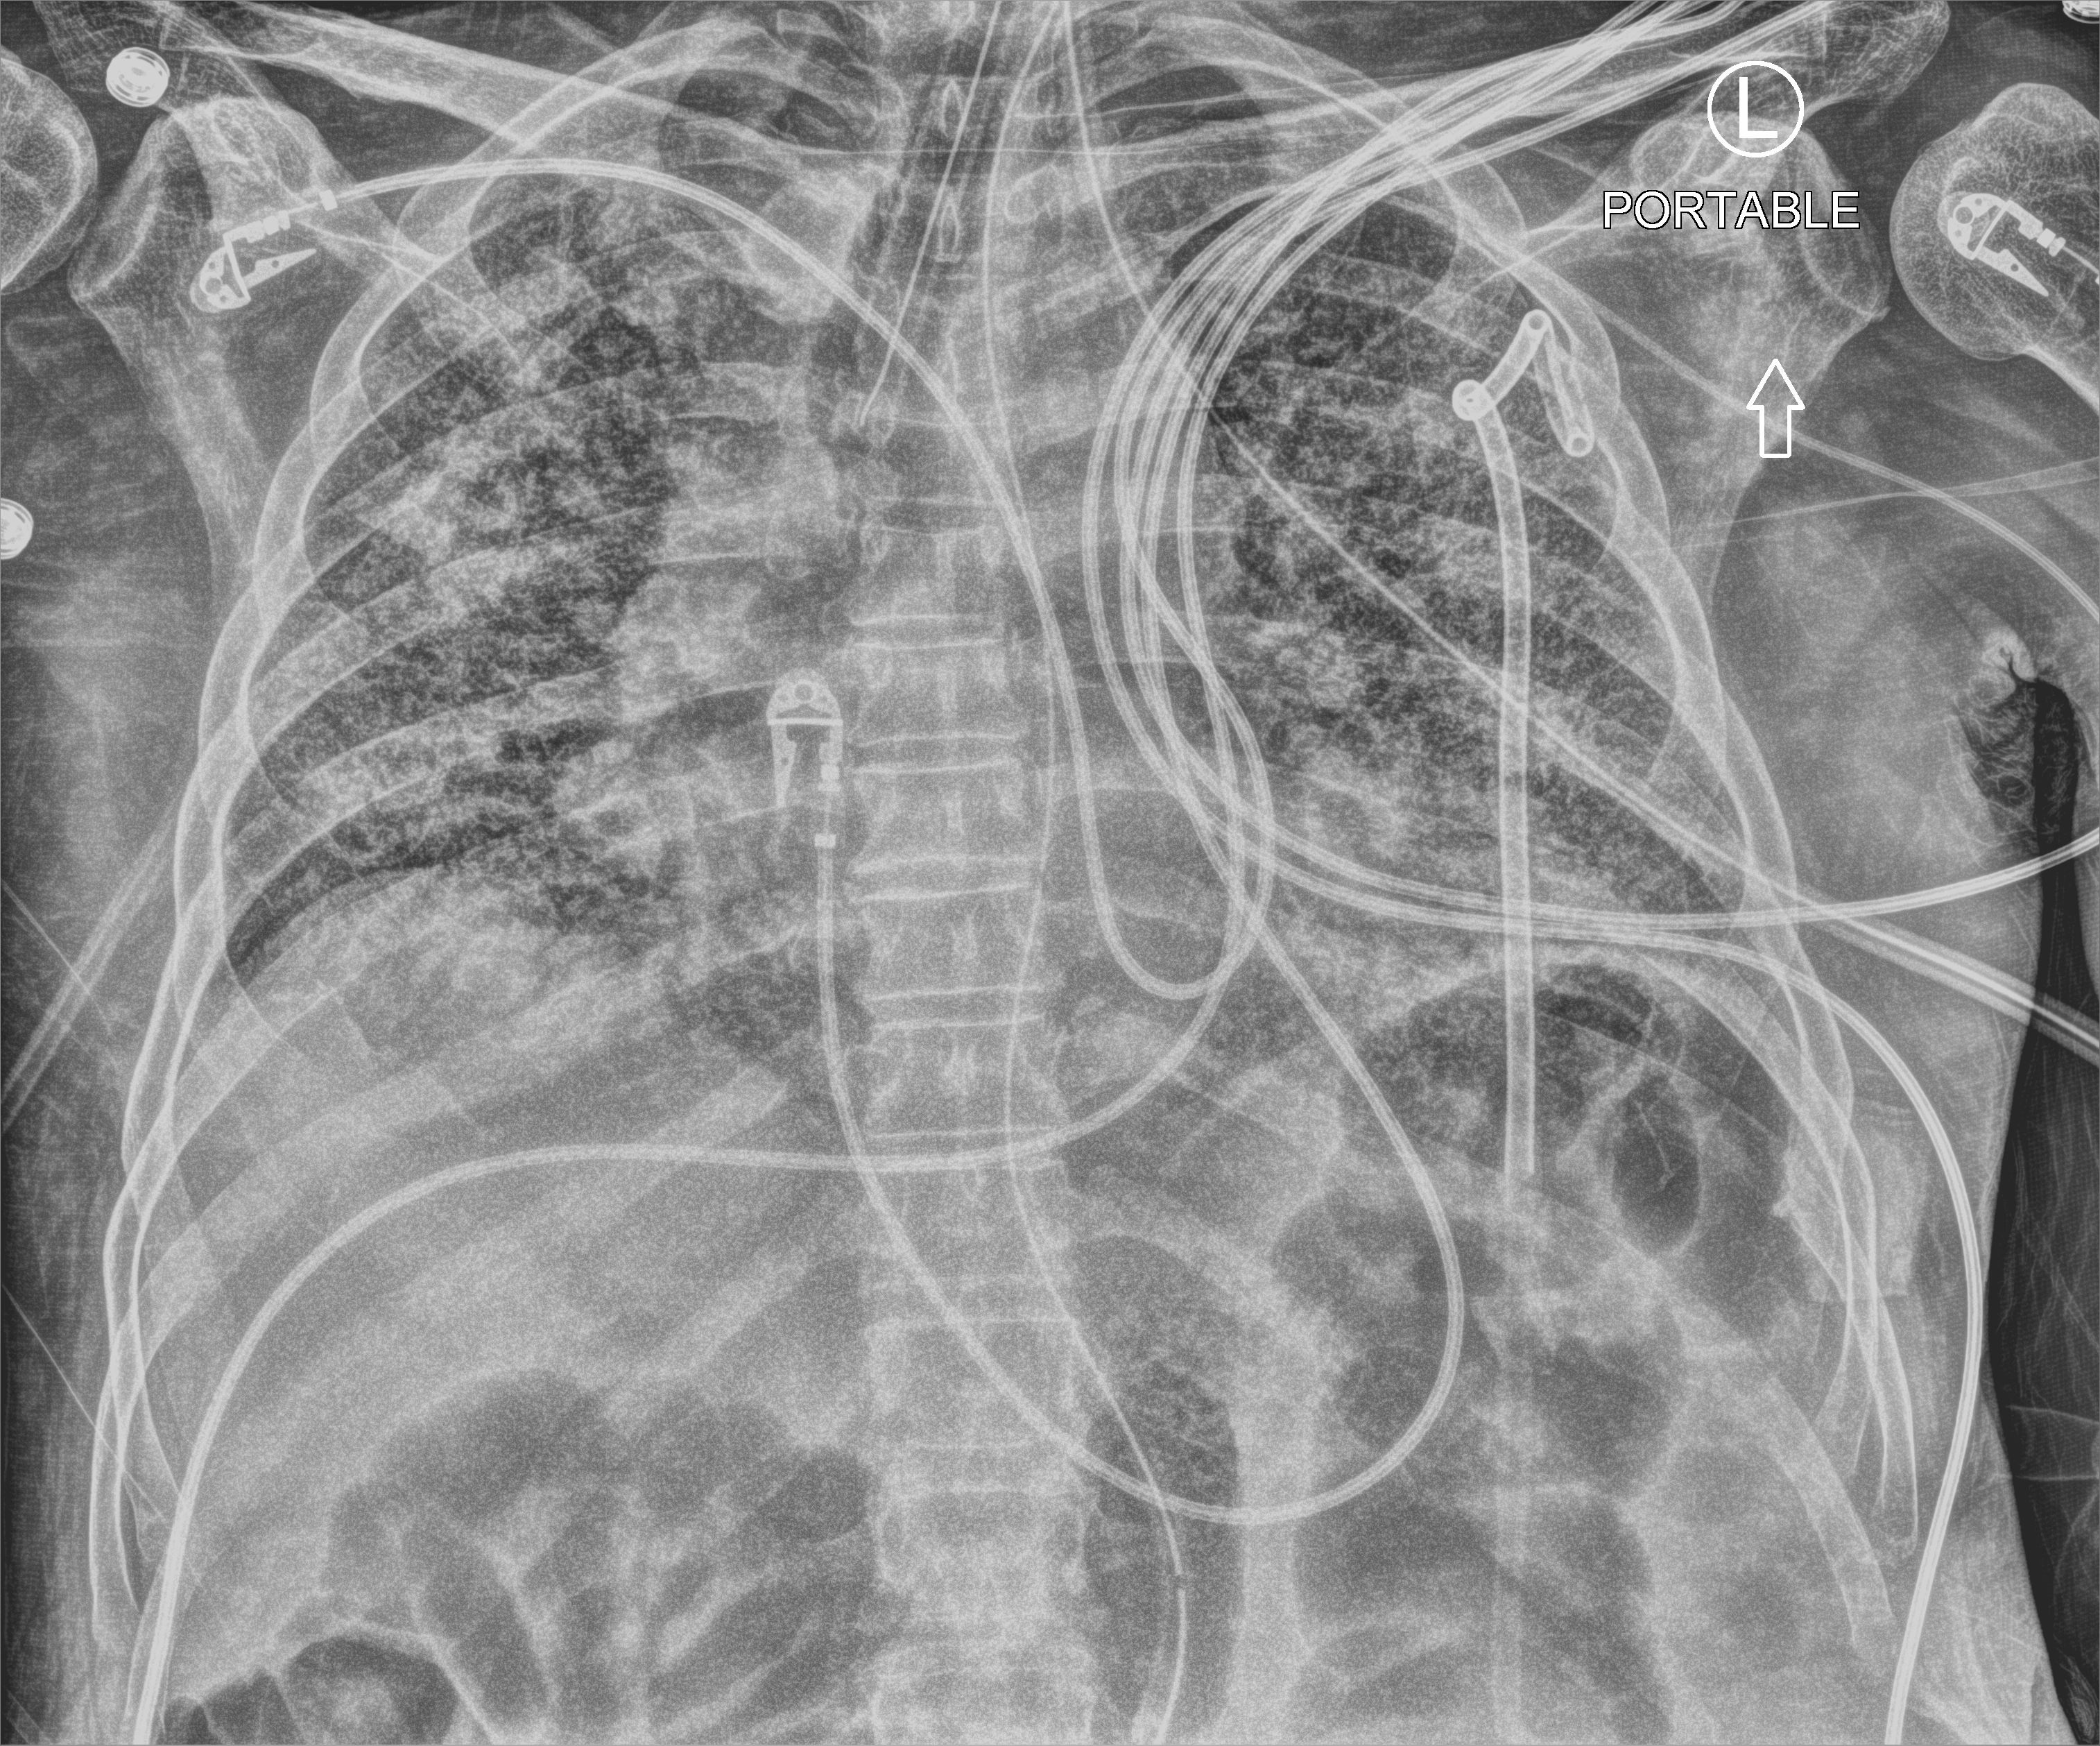
Chest X-ray (portable); anteroposterior (AP) projection. Patient hospitalised with COVID-19; male, aged 60–74 years.
Admission-level facts for this patient (not findings on this image; timing relative to this image not recorded):
- mechanically ventilated during this hospital stay: yes